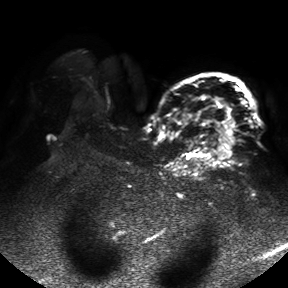
Breast MRI, one axial slice. Slice 33 of 50 in the series (ordered by position). Diffusion-weighted series; image 2 of 4 stored at this slice position (different b-values; order by instance number). 1.5 T. 288 × 288 image matrix, field of view 390 × 390 mm. Female patient.
Outlined on this slice (manually delineated by an expert):
- tumour on diffusion-weighted imaging: bounding box [x1, y1, x2, y2] px = [215, 98, 235, 159]